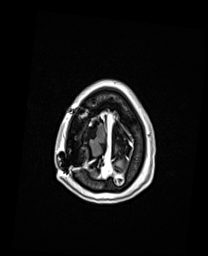
Brain MRI from a brain-tumour surgery series, one axial slice. Slice 27 of 192 in the series (ordered by position). T1-weighted post-contrast. 208 × 256 image matrix. Case-level facts recorded for this patient, not image findings: histopathology: Oligodendroglioma; WHO grade: 3; IDH mutation: yes; tumour location: Right Frontal.
Outlined on this slice (expert manual segmentation):
- previous resection cavity: bounding box (x1, y1, x2, y2) in pixels: (72, 121, 99, 142)